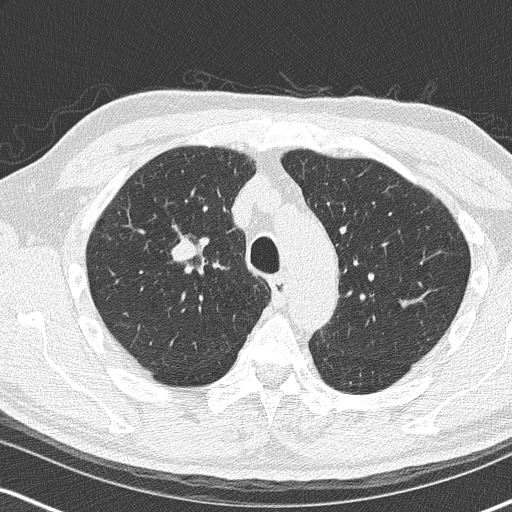
Axial slice from a low-dose chest CT screening exam. Second screening round (one year after baseline). Lung window (W 1500 / L -600 HU). 2 mm slice thickness. Slice 57 of 170 in the series. 512 × 512 image matrix, field of view 320 × 320 mm. Male participant, aged 68 years at enrolment. Current smoker at enrolment.
- Expert-annotated lung lesion, bounding box <152,227,216,289> (left, top, right, bottom; pixels).
- Screening reader's record for this exam (one nodule recorded; not confirmed to be the boxed lesion): non-calcified nodule or mass ≥4 mm, right upper lobe, 18 × 15 mm, smooth margins, soft tissue attenuation, pre-existing on the prior screen: no.
- Official screen result: positive, change unspecified: nodule(s) >= 4 mm or enlarging nodule(s), mass(es), or other non-specific abnormalities suspicious for lung cancer.
- Later outcome: lung cancer diagnosed 136 days after this screen — small cell carcinoma, NOS, right upper lobe, stage IIIB (AJCC 6th edition), 20 mm at pathology.